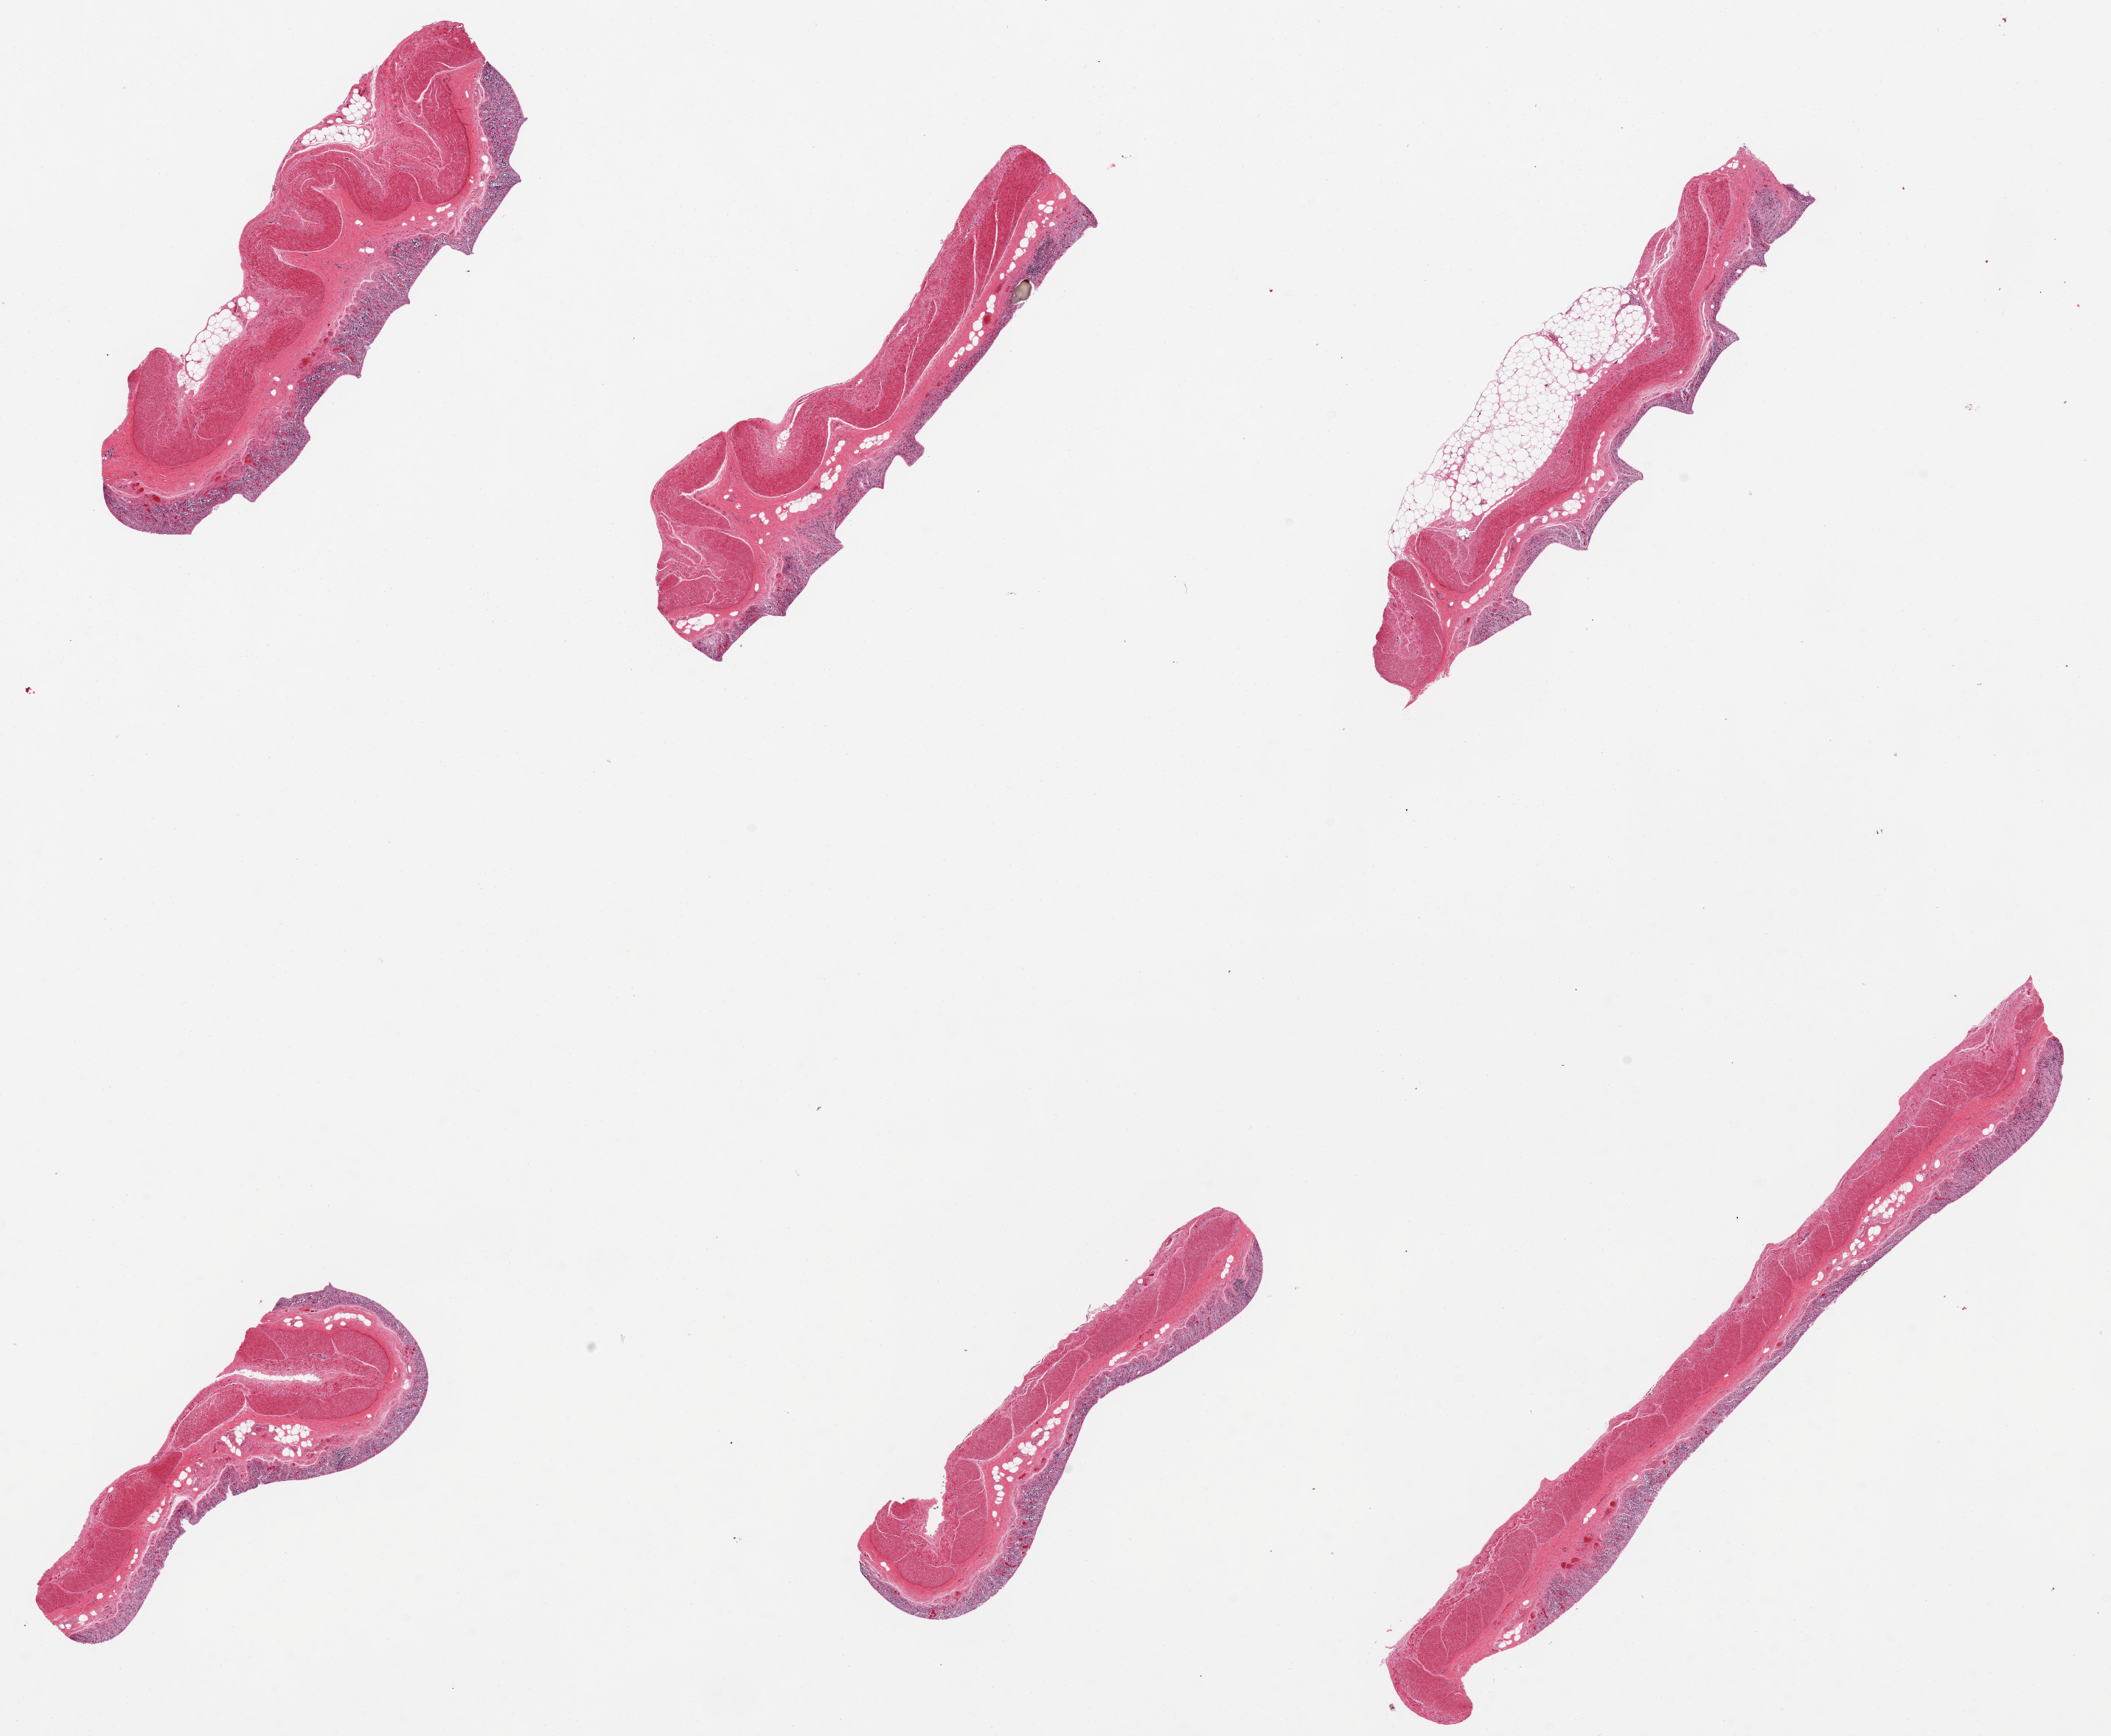
Digitized hematoxylin and eosin (H&E)-stained section, whole scanned area (about 22.6 x 18.6 mm) shown as a low-resolution overview. PAXgene-fixed paraffin-embedded (PFPE) section. Sampled site (target tissue): transverse colon. Donor tissue sample. Donor: male.
Review note (as recorded): 6 pieces; mucosa=3, muscle=1.